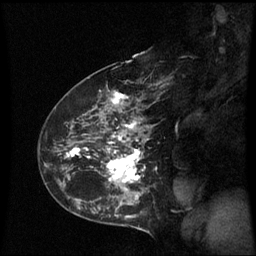
Breast MRI (dynamic contrast-enhanced), one sagittal slice; position 40 of 60 along the scan axis; dynamic contrast-enhanced series, image 2 of 3 at this slice position (ordered by acquisition); 1.5 T; TE 4.2 ms, TR 8.9 ms; 2.3 mm slice thickness; 256 × 256 image matrix, field of view 210 × 210 mm. Patient: female, 43 years. From the clinical record (not read from this slice): setting: breast cancer imaged before/during neoadjuvant chemotherapy; receptor status: HER2-positive.
Outlined on this slice (semi-automatically segmented with operator editing):
- analysis volume of interest (the breast-tissue region the enhancement analysis was run in; not a lesion): bounding box (x1, y1, x2, y2) in pixels: (56, 80, 158, 195)
- tumour enhancement mask (voxels above the 70 % enhancement threshold inside the analysis volume of interest): (67, 93, 149, 191)